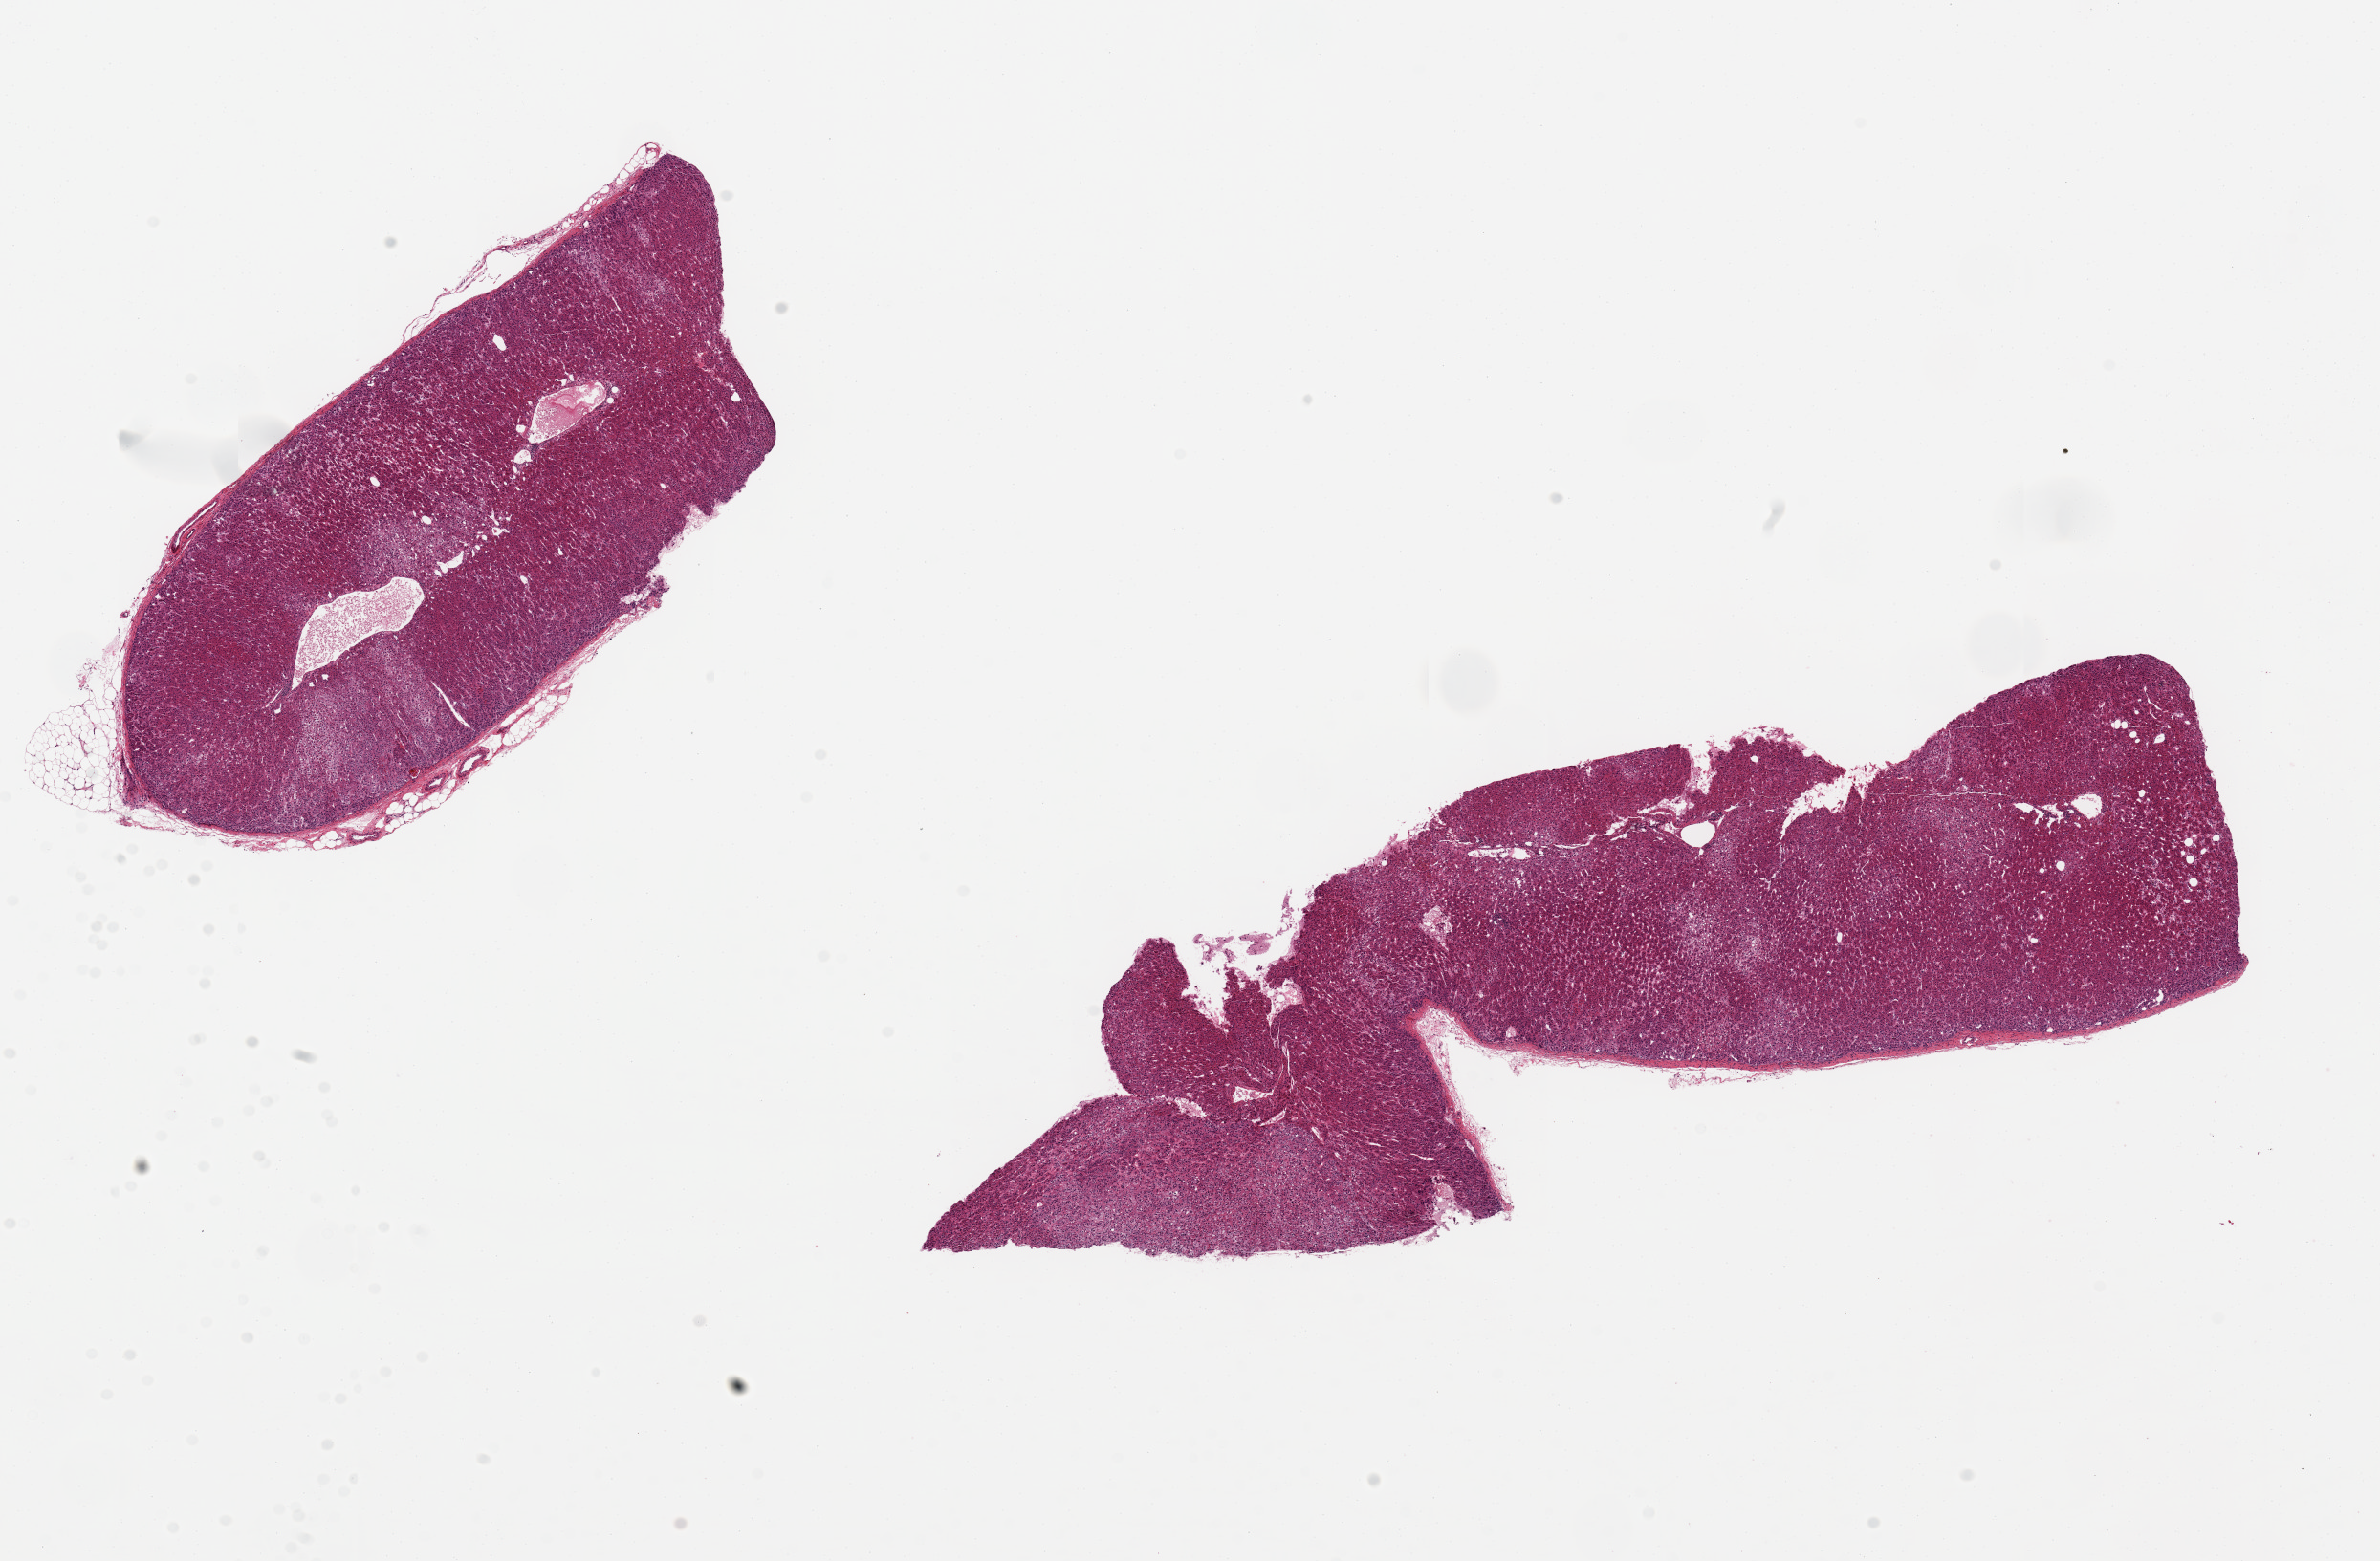
Whole-slide image, hematoxylin and eosin (H&E) stain, brightfield, a low-resolution overview of the entire scanned area, about 19.7 x 12.9 mm; PAXgene-fixed paraffin-embedded (PFPE) section; section of adrenal gland (target tissue); donor tissue sample.
• review note (as recorded): 2 ~3x8mm pieces. All cortex, well-preserved